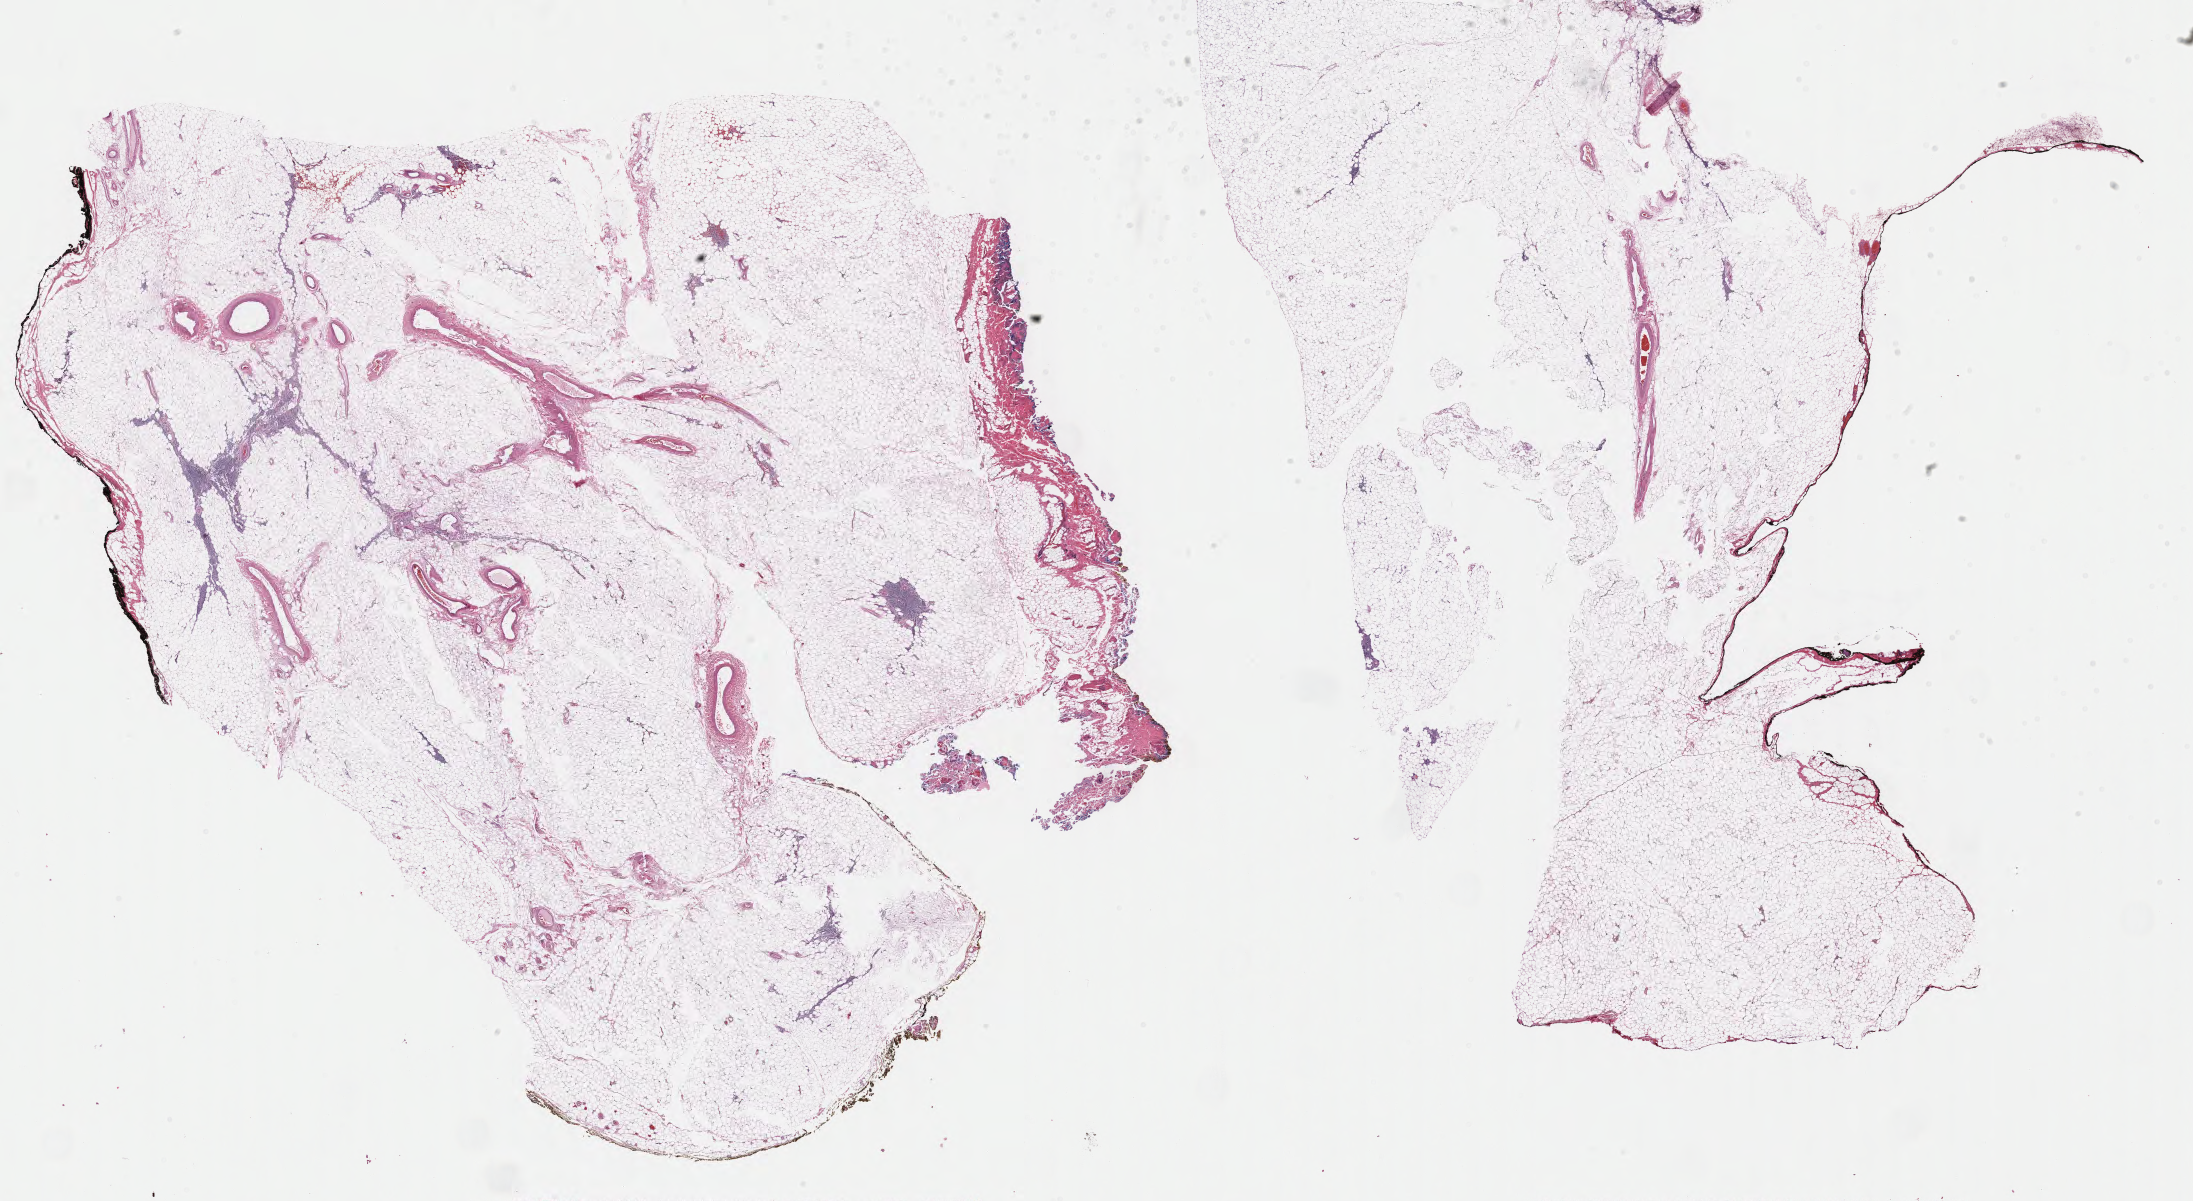
Whole-slide histology image, H&E, shown as a low-resolution overview of the whole scanned area (about 34.8 x 19.0 mm), formalin-fixed paraffin-embedded (FFPE) diagnostic section, thymus, primary tumour sample. Male patient; age at initial diagnosis 52 years.
Pathologic diagnosis: Thymoma, type A, malignant.